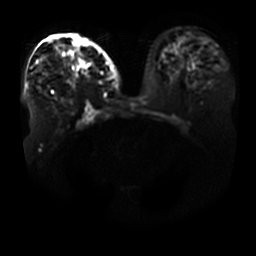
Breast MRI, one axial slice; position 21 of 41 along the scan axis; diffusion-weighted series; image 2 of 4 stored at this slice position (different b-values; order by instance number); 3 T; 5 mm slice thickness; 256 × 256 image matrix, field of view 400 × 400 mm. Female patient.
Annotated regions visible in this slice (manually delineated by an expert):
- tumour on diffusion-weighted imaging: bounding box (x1, y1, x2, y2) in pixels: (94, 67, 99, 73)